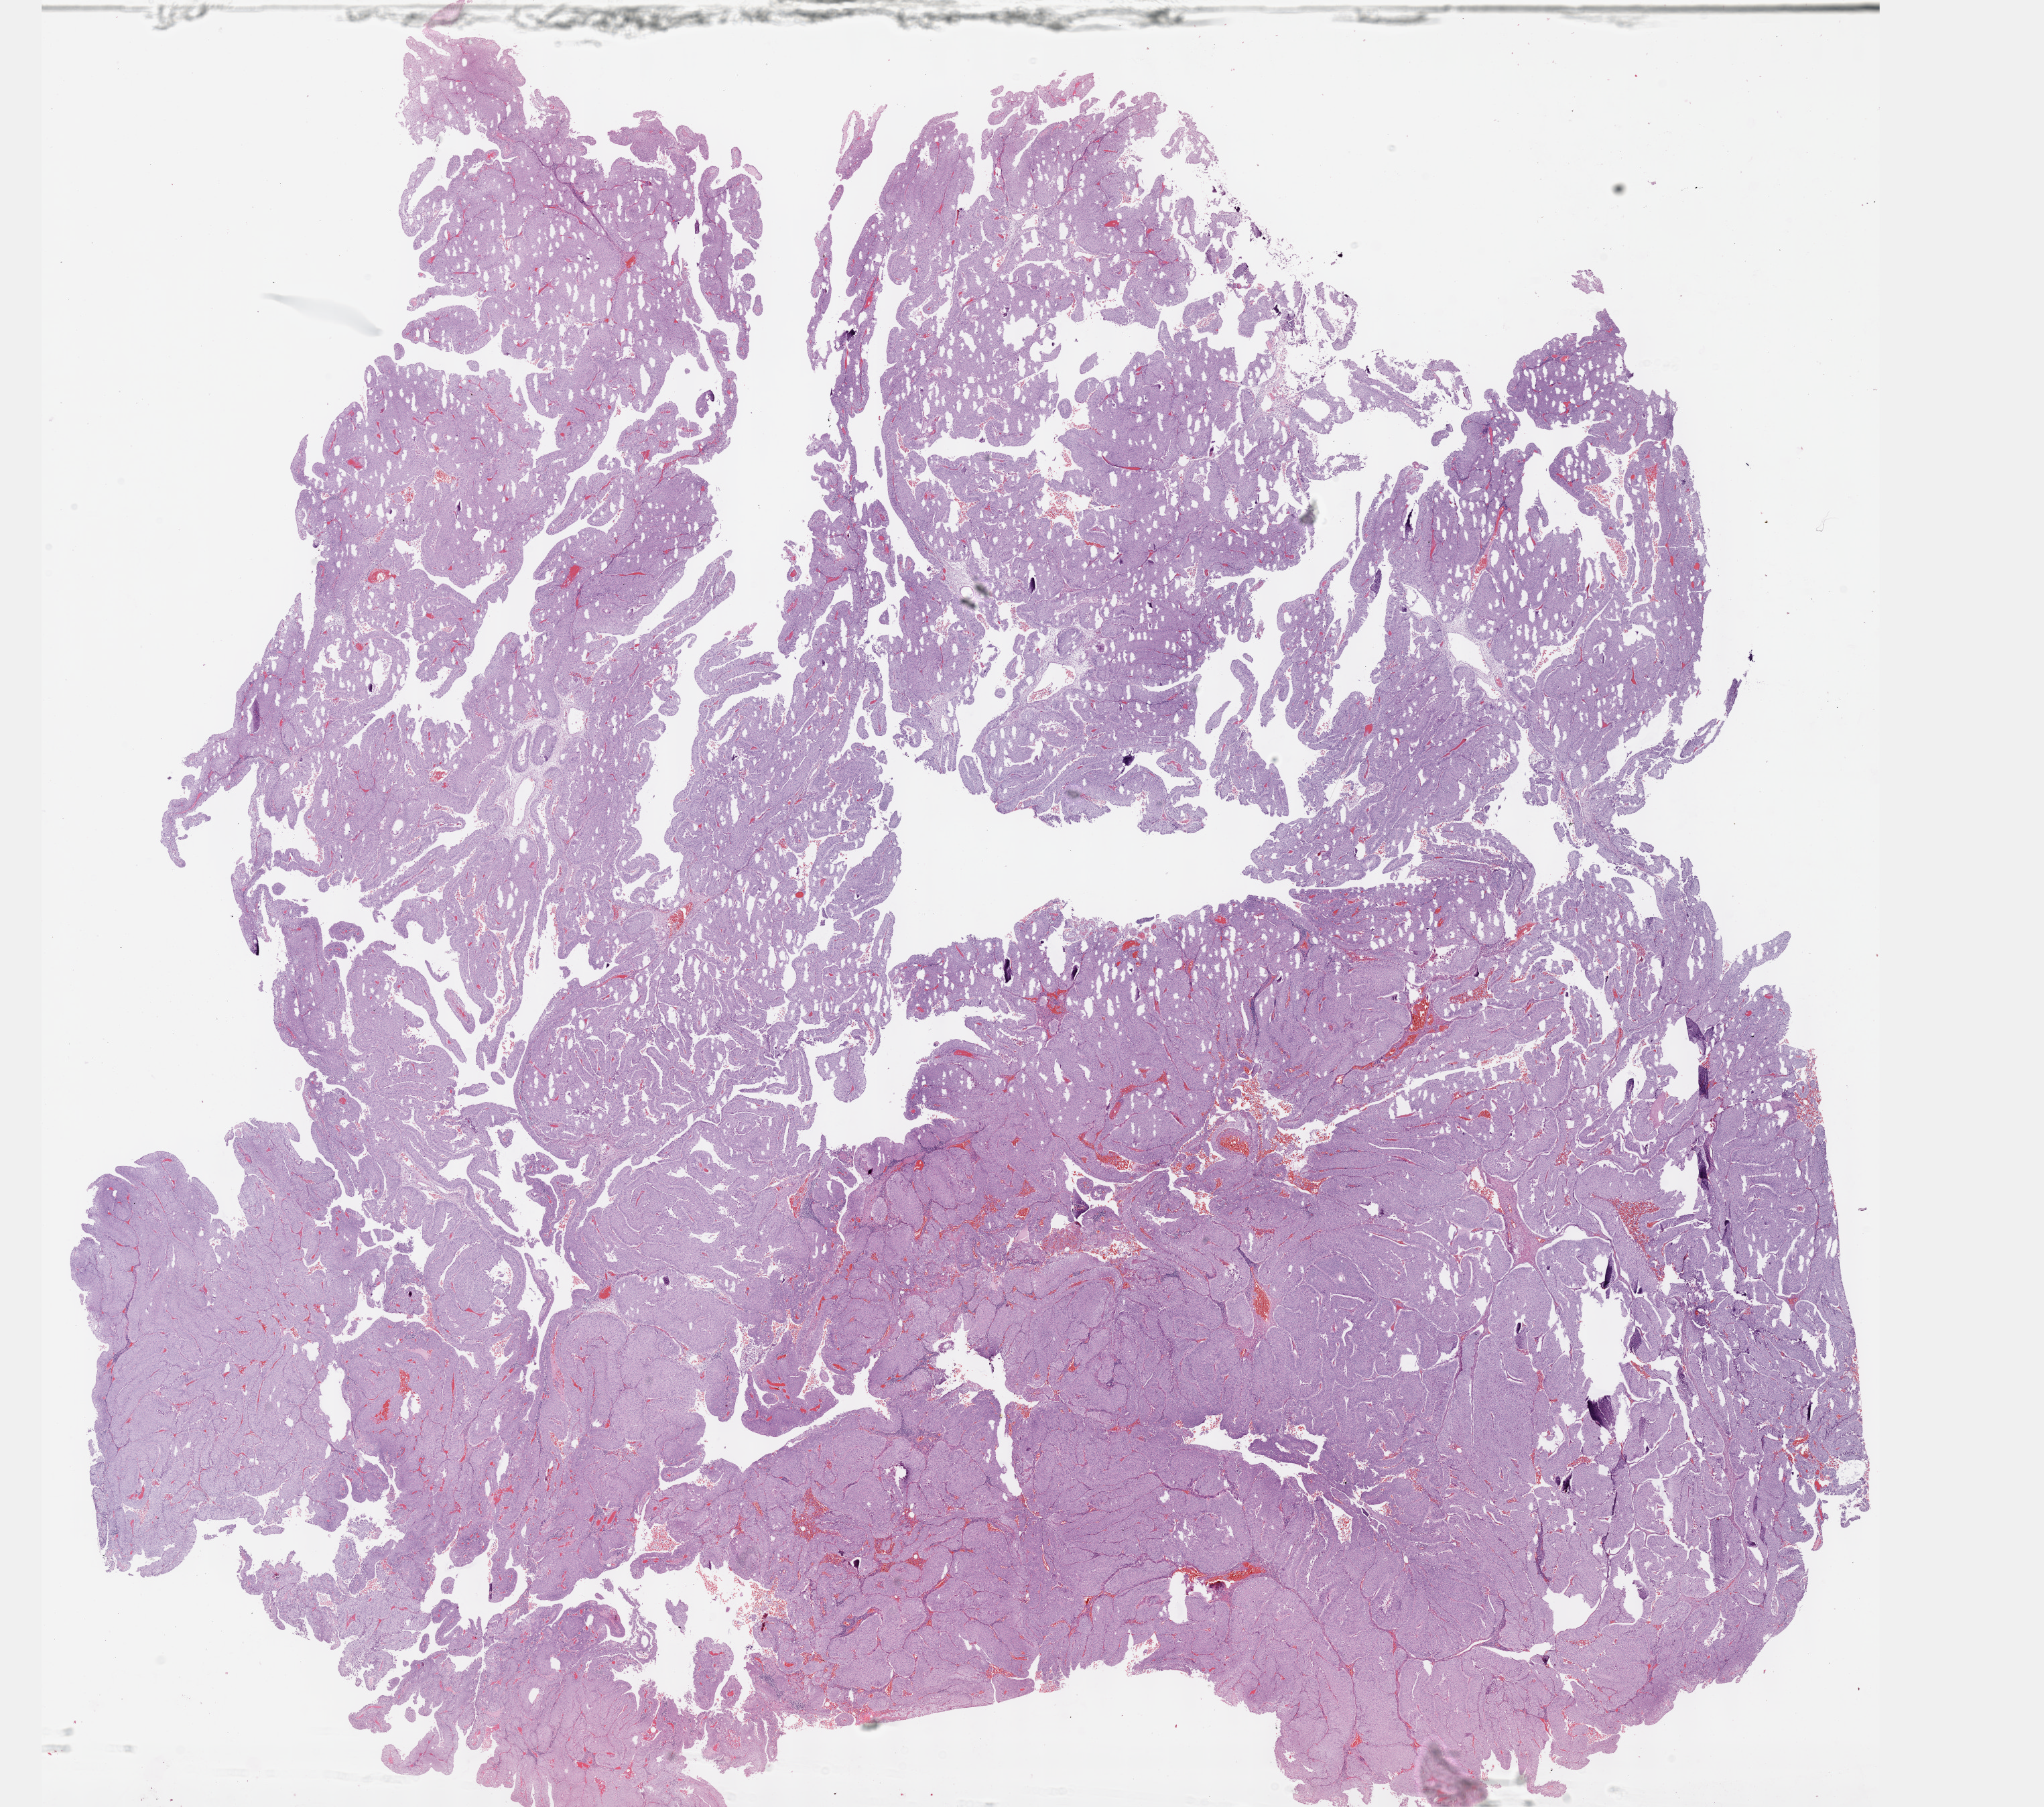
Digitized Hematoxylin and eosin (H&E) stained tissue section (whole slide), a low-resolution overview of the entire scanned area, about 24.6 x 21.8 mm; FFPE section; primary tumour sample from the bladder. Patient: male, age at initial diagnosis 50 years. Histologic grade: high grade.
Diagnosis: Papillary transitional cell carcinoma. AJCC pathologic stage: I (6th edition).